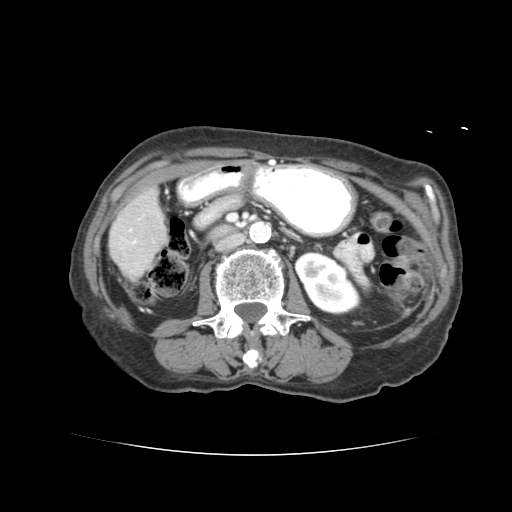
Contrast-enhanced abdominal CT (liver protocol), one axial slice; position 14 of 77 along the scan axis; reconstruction kernel STANDARD; 120 kVp; soft-tissue window (W 400 / L 40 HU); 2.5 mm slice thickness; 512 × 512 image matrix. Case-level facts recorded for this patient, not image findings: diagnosis: hepatocellular carcinoma (patient treated with transarterial chemoembolisation; whether this scan precedes or follows treatment is not stated here); TNM stage (as recorded): Stage-I.
Annotated regions visible in this slice (semi-automatic segmentation, software-assisted and operator-edited):
- liver parenchyma outside the tumour (the mass and vessels are separate outlines, so this box may not span the whole liver): bounding box [x1, y1, x2, y2] px = [108, 172, 166, 272]
- liver vessels: [129, 209, 154, 245]